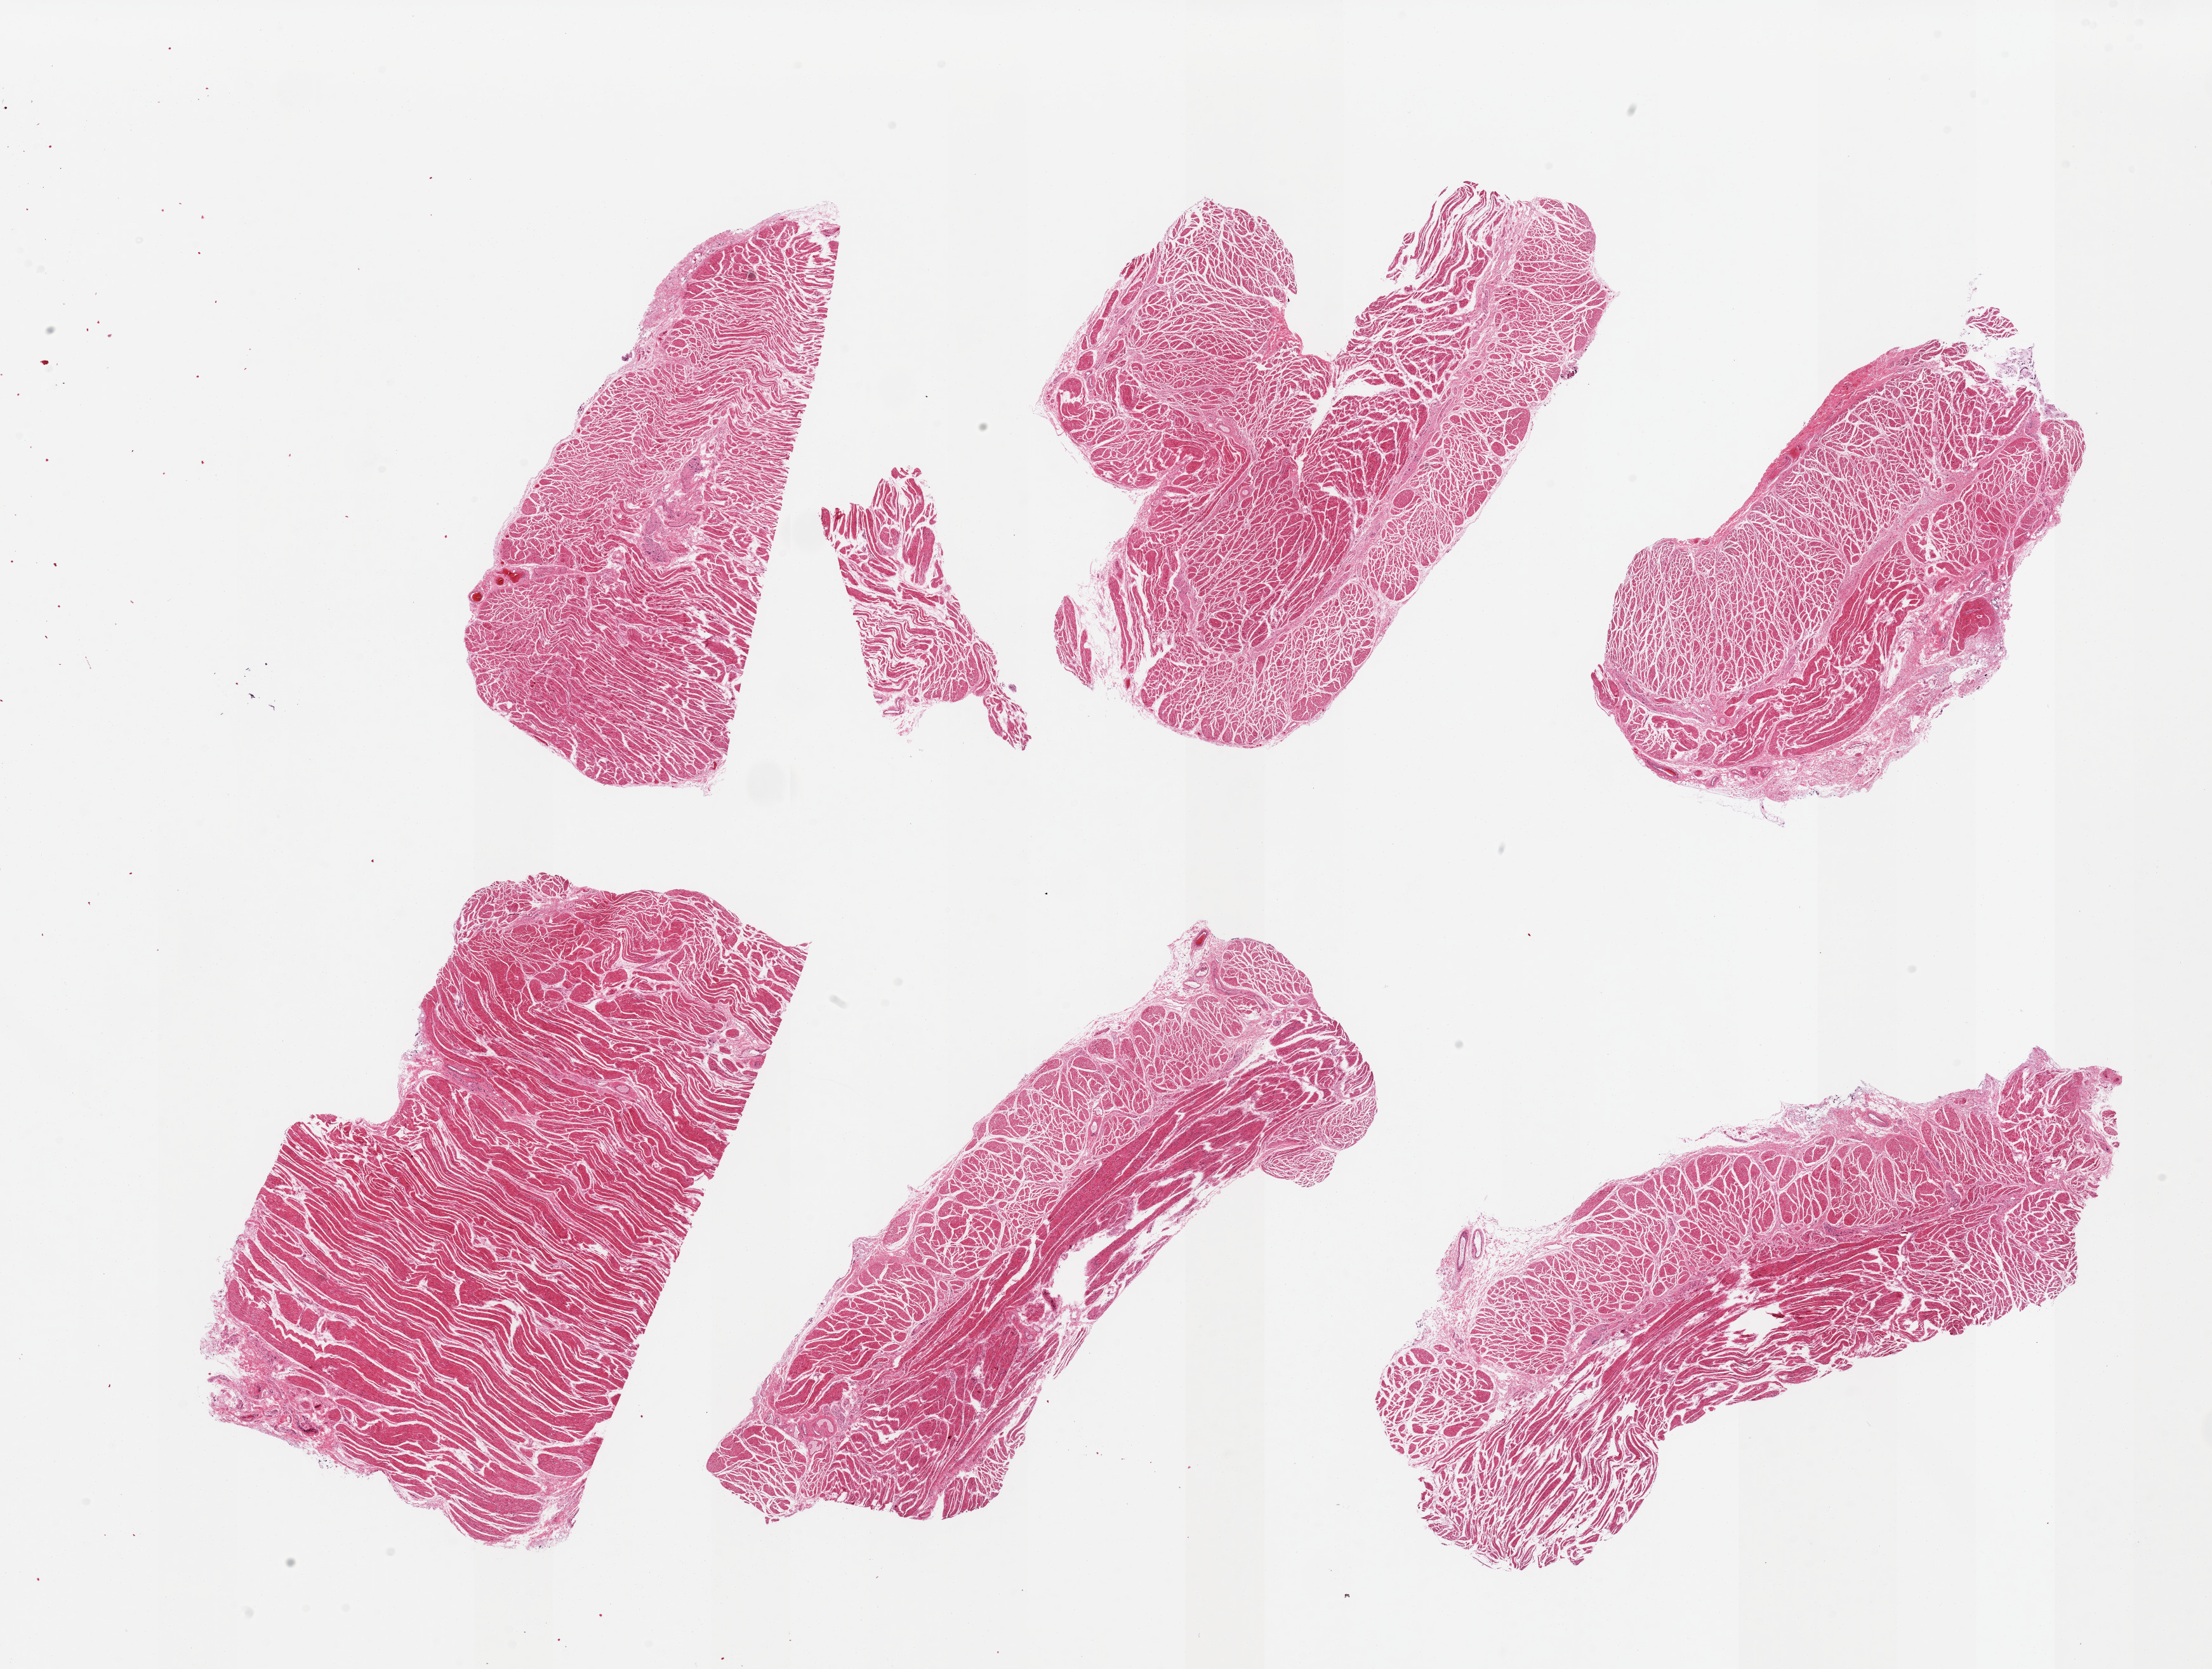
Digitized hematoxylin and eosin (H&E)-stained section — low-resolution overview of the scanned area, about 27.6 x 20.8 mm (acquisition: 20x scan). PAXgene-fixed, paraffin-embedded tissue. Sampled site (target tissue): gastroesophageal junction. Donor tissue sample. Donor sex: male.
Review note (as recorded): 6 pieces; well trimmed target muscularis.